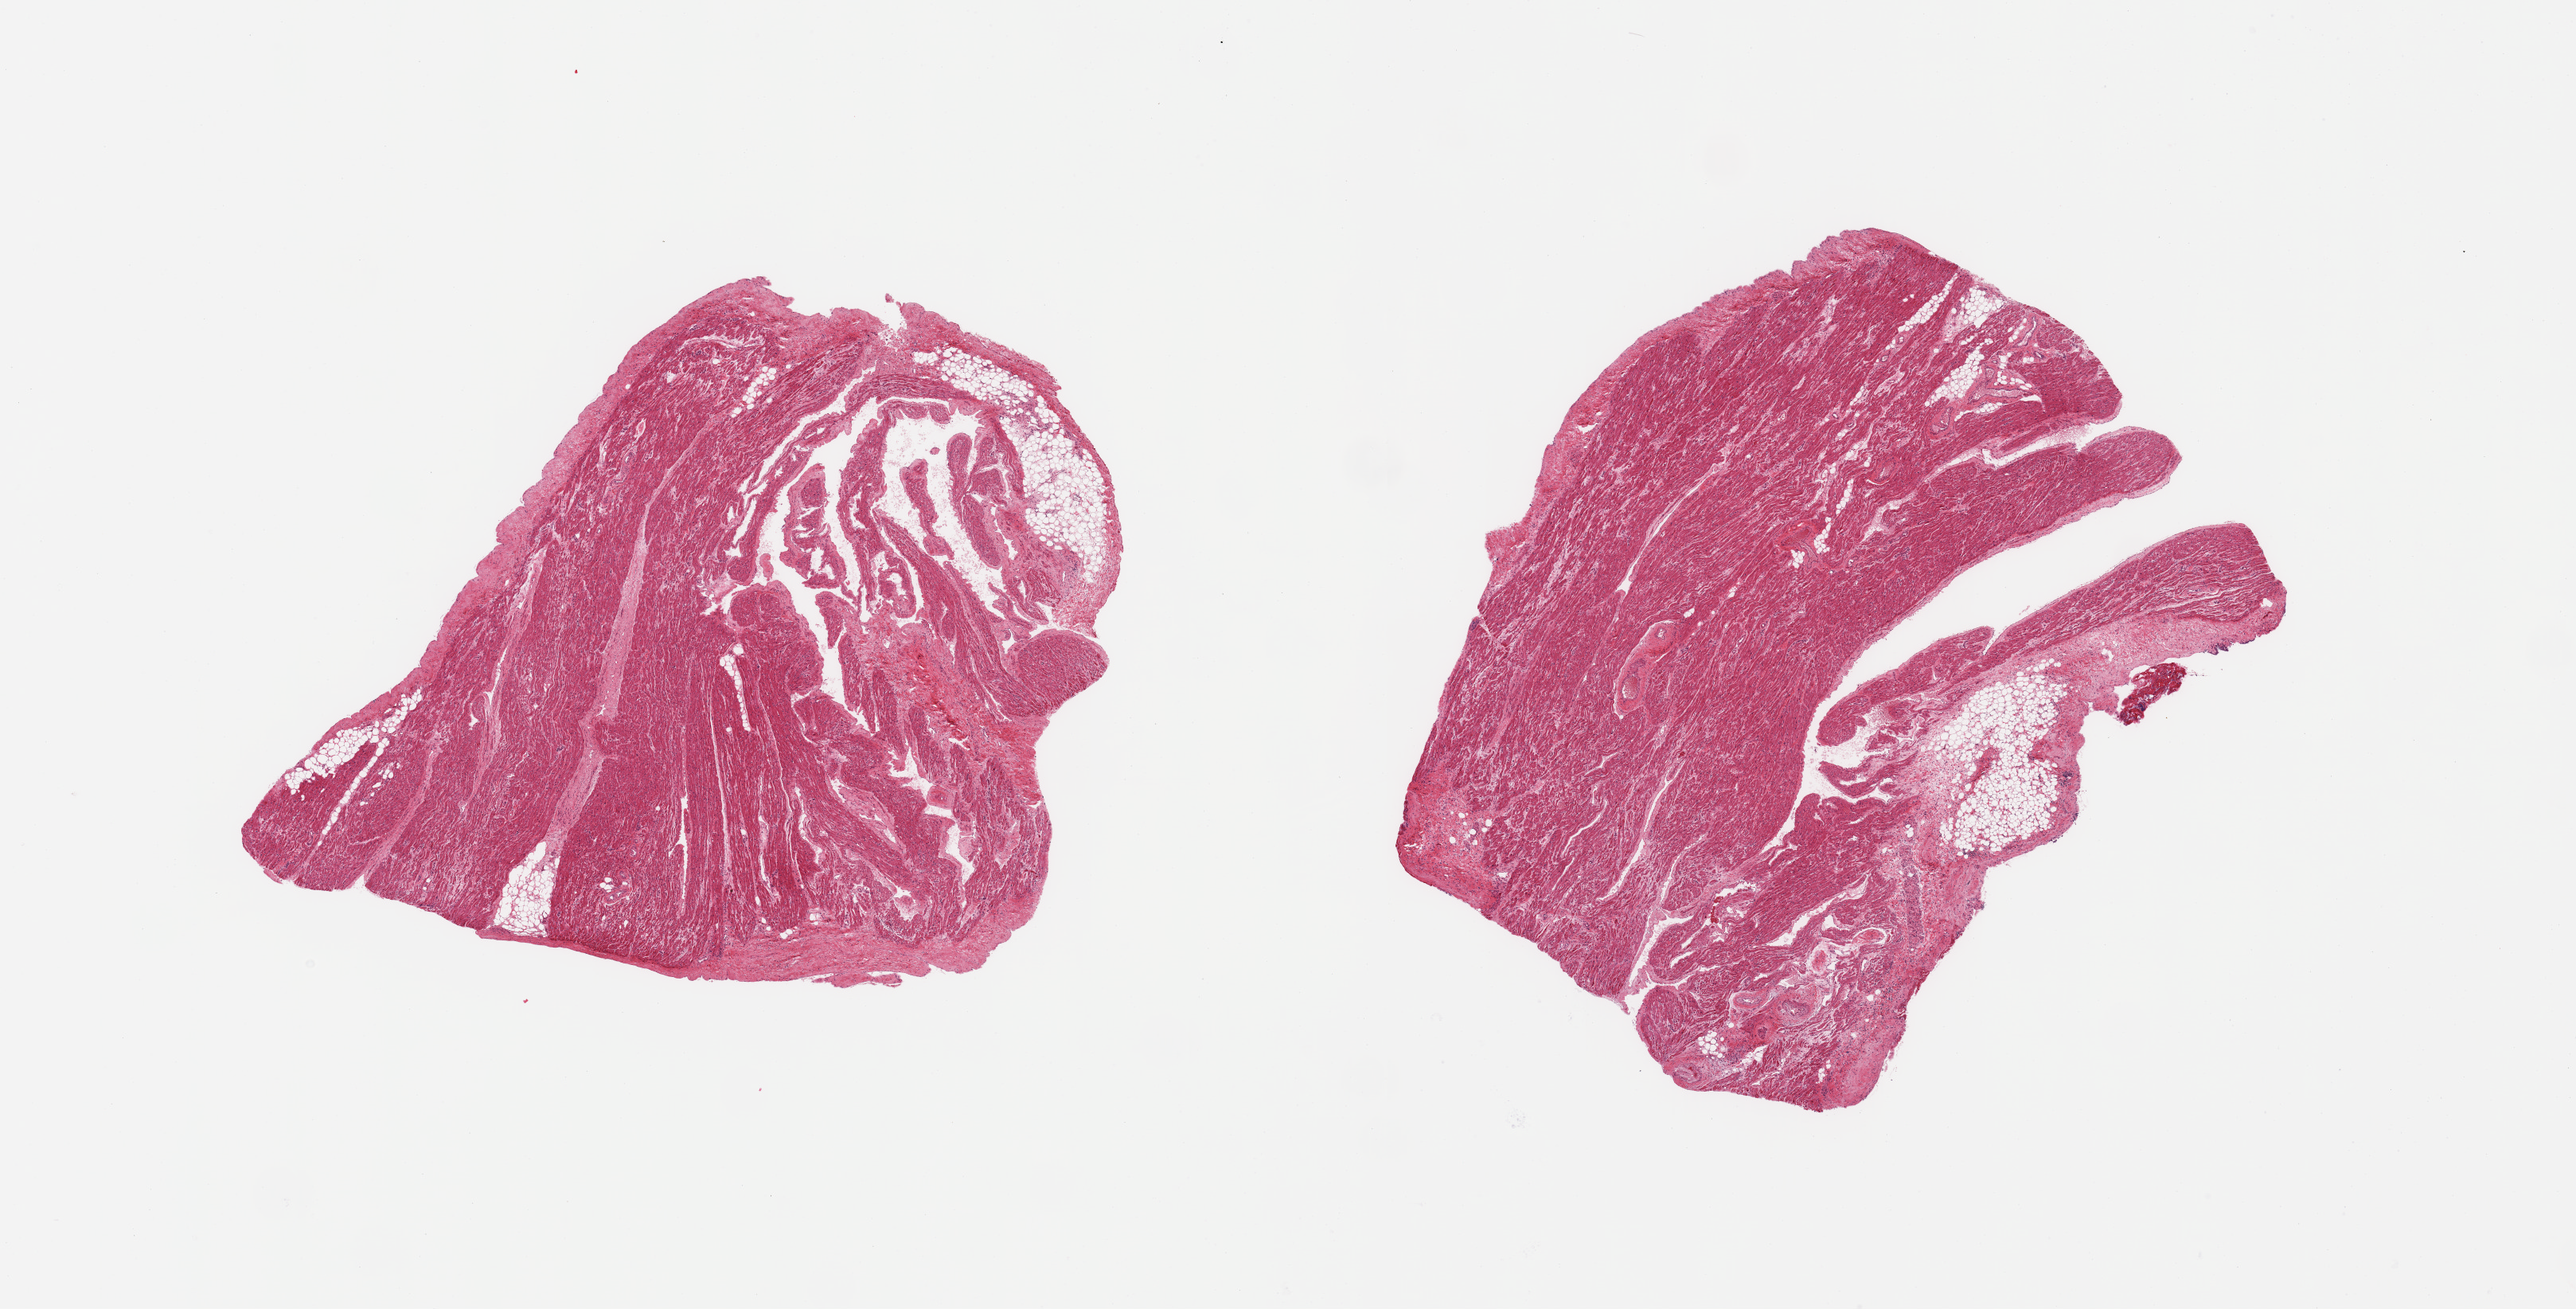
Digitized H&E-stained section, a low-resolution overview of the entire scanned area, about 25.6 x 13.0 mm (slide scanned at 20x); PAXgene-fixed paraffin-embedded (PFPE) section; sampled site (target tissue): auricular appendage; donor tissue sample. Donor: female.
• pathologist's review note for this sample: 2 pieces, no abnormalities